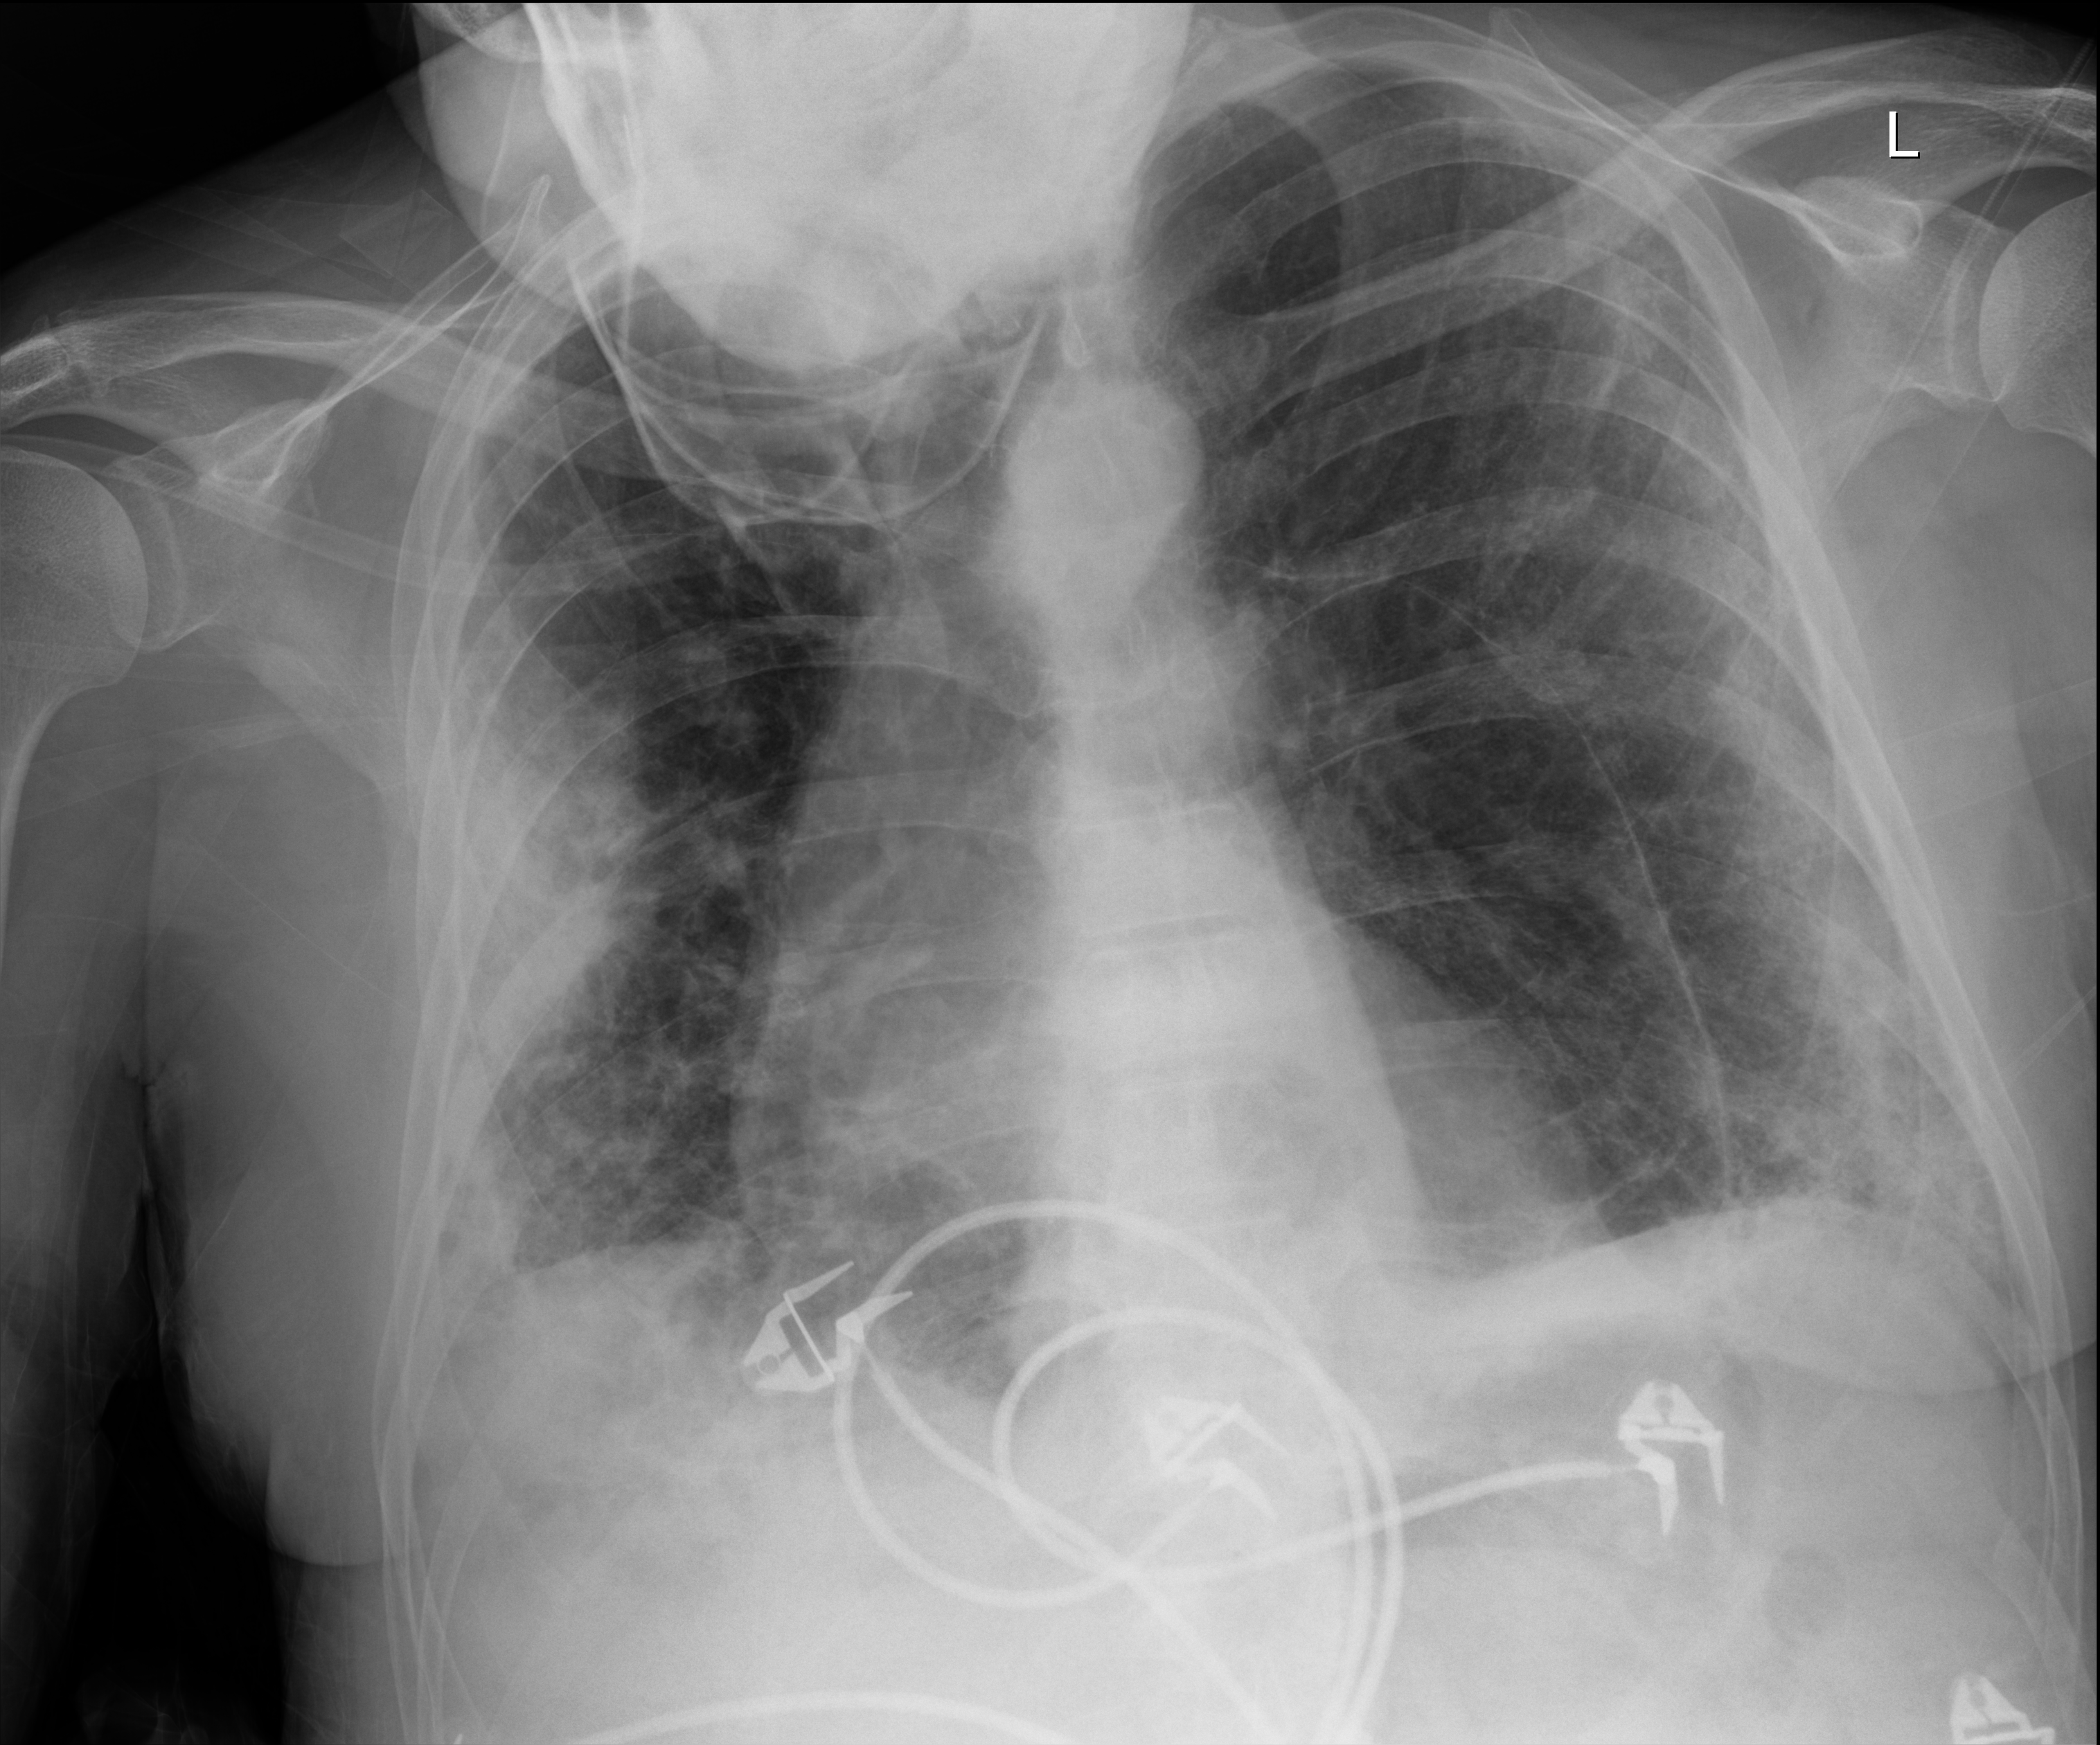
Portable chest radiograph. Male patient hospitalised with COVID-19, age 60–74 years.
Admission-level facts for this patient (not findings on this image; timing relative to this image not recorded): admitted to intensive care during this hospital stay: no.